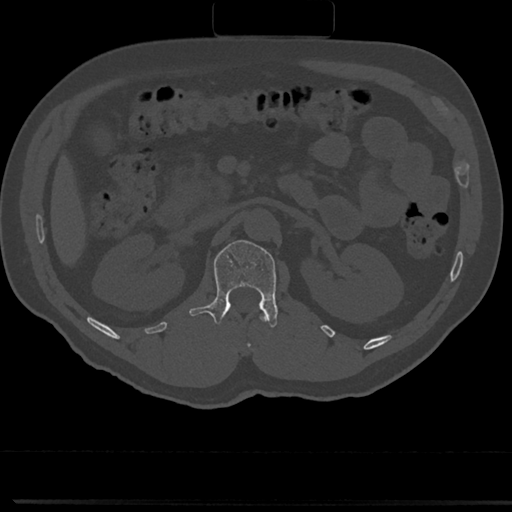
CT including the spine, one axial slice; position 95 of 817 along the scan axis; reconstruction kernel Br40s/3; bone window (W 1800 / L 400 HU); 0.5 mm slice thickness; 512 × 512 image matrix. Male patient, age 61 years. From the clinical record (not read from this slice): primary cancer: prostate.
Annotated regions visible in this slice (semi-automatic segmentation, software-assisted and operator-edited):
- L1 vertebra: bounding box <191,240,279,327> (left, top, right, bottom; pixels)